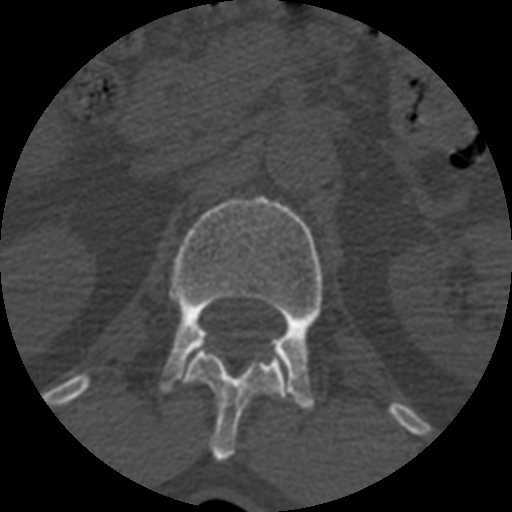
CT including the spine, one axial slice; position 370 of 399 along the scan axis; reconstruction kernel STANDARD; bone window (W 1800 / L 400 HU); 1.25 mm slice thickness; 512 × 512 image matrix, field of view 160 × 160 mm. Patient age 71 years. From the clinical record (not read from this slice): primary cancer: prostate.
Structures marked on this image (semi-automatic segmentation, software-assisted and operator-edited):
- L1 vertebra: bounding box [x1, y1, x2, y2] px = [159, 196, 323, 410]
- T12 vertebra: [184, 348, 290, 461]